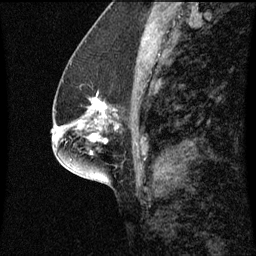
Breast MRI (dynamic contrast-enhanced), one sagittal slice. Position 27 of 60 along the scan axis. Dynamic contrast-enhanced series, image 2 of 3 at this slice position (ordered by acquisition). 1.5 T. TE 4.2 ms, TR 8.9 ms. 2 mm slice thickness. 256 × 256 image matrix, field of view 200 × 200 mm. Patient: female, 57 years. From the clinical record (not read from this slice): setting: breast cancer imaged before/during neoadjuvant chemotherapy; receptor status: HR-positive, HER2-negative.
Annotated regions visible in this slice (semi-automatically segmented with operator editing):
- analysis volume of interest (the breast-tissue region the enhancement analysis was run in; not a lesion): bounding box (x1, y1, x2, y2) in pixels: (82, 92, 124, 125)
- tumour enhancement mask (voxels above the 70 % enhancement threshold inside the analysis volume of interest): (94, 94, 105, 115)